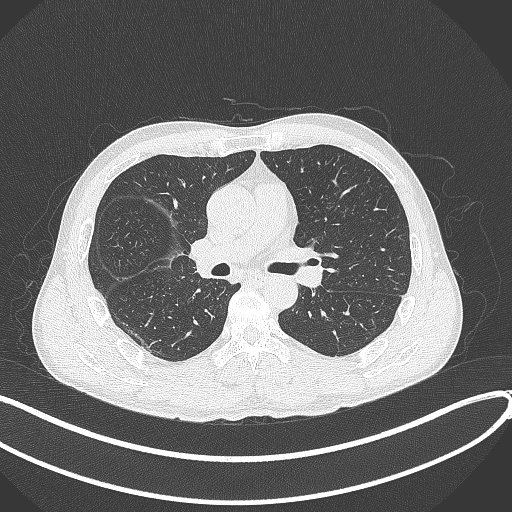
Chest CT, one axial slice. Slice 222 of 409 in the series (ordered by position). 120 kVp. Lung window (W 1500 / L -600 HU). 1 mm slice thickness. 512 × 512 image matrix, field of view 400 × 400 mm. Patient: male, 53 years. From the clinical record (not read from this slice): clinical TNM (as recorded): T1b N0 M0.
Annotated regions visible in this slice (rectangle marked by the reading radiologist):
- lung tumour (recorded histology: squamous cell carcinoma): bounding box [x1, y1, x2, y2] px = [183, 230, 223, 285]